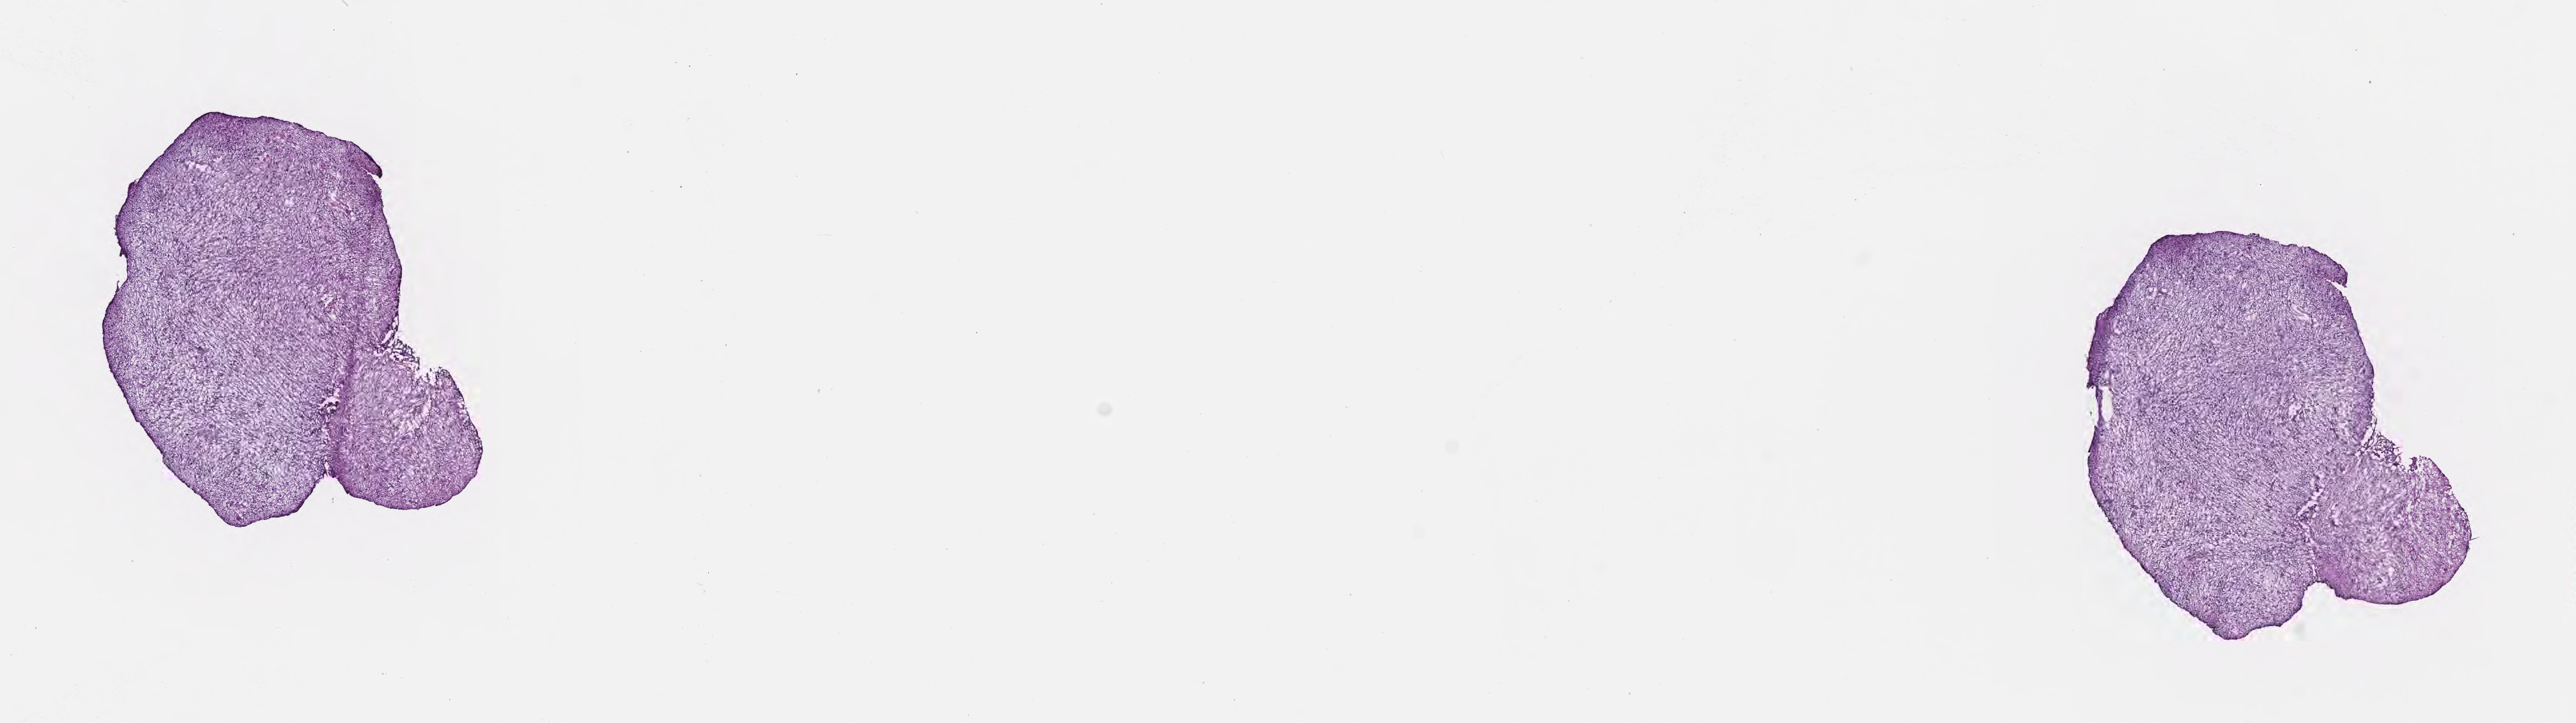
H&E whole-slide image — low-resolution overview of the scanned area, about 15.6 x 4.4 mm, frozen section, primary tumor, site: brain. Female patient; age at initial diagnosis 63 years. Pathologist review of this section (percent, as recorded): tumor cells 62%, tumor nuclei 81%, stromal cells 24%, necrosis 0%, normal cells 14%. Inflammatory infiltration, as recorded: lymphocyte infiltration 0%, monocyte infiltration 0%, neutrophil infiltration 0%.
Diagnosis: Glioblastoma, NOS. Section: top of the tissue portion.